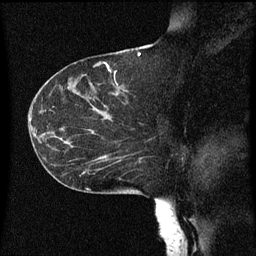
Breast MRI (dynamic contrast-enhanced), one sagittal slice. Dynamic contrast-enhanced series, image 2 of 3 at this slice position (ordered by acquisition). 1.5 T. TE 4.2 ms, TR 8 ms. 2 mm slice thickness. 256 × 256 image matrix, field of view 200 × 200 mm. Patient: female, 55 years.
Outlined on this slice (semi-automatically segmented with operator editing):
- analysis volume of interest (the breast-tissue region the enhancement analysis was run in; not a lesion): bounding box (x1, y1, x2, y2) in pixels: (46, 124, 151, 183)
- tumour enhancement mask (voxels above the 70 % enhancement threshold inside the analysis volume of interest): (100, 156, 109, 169)